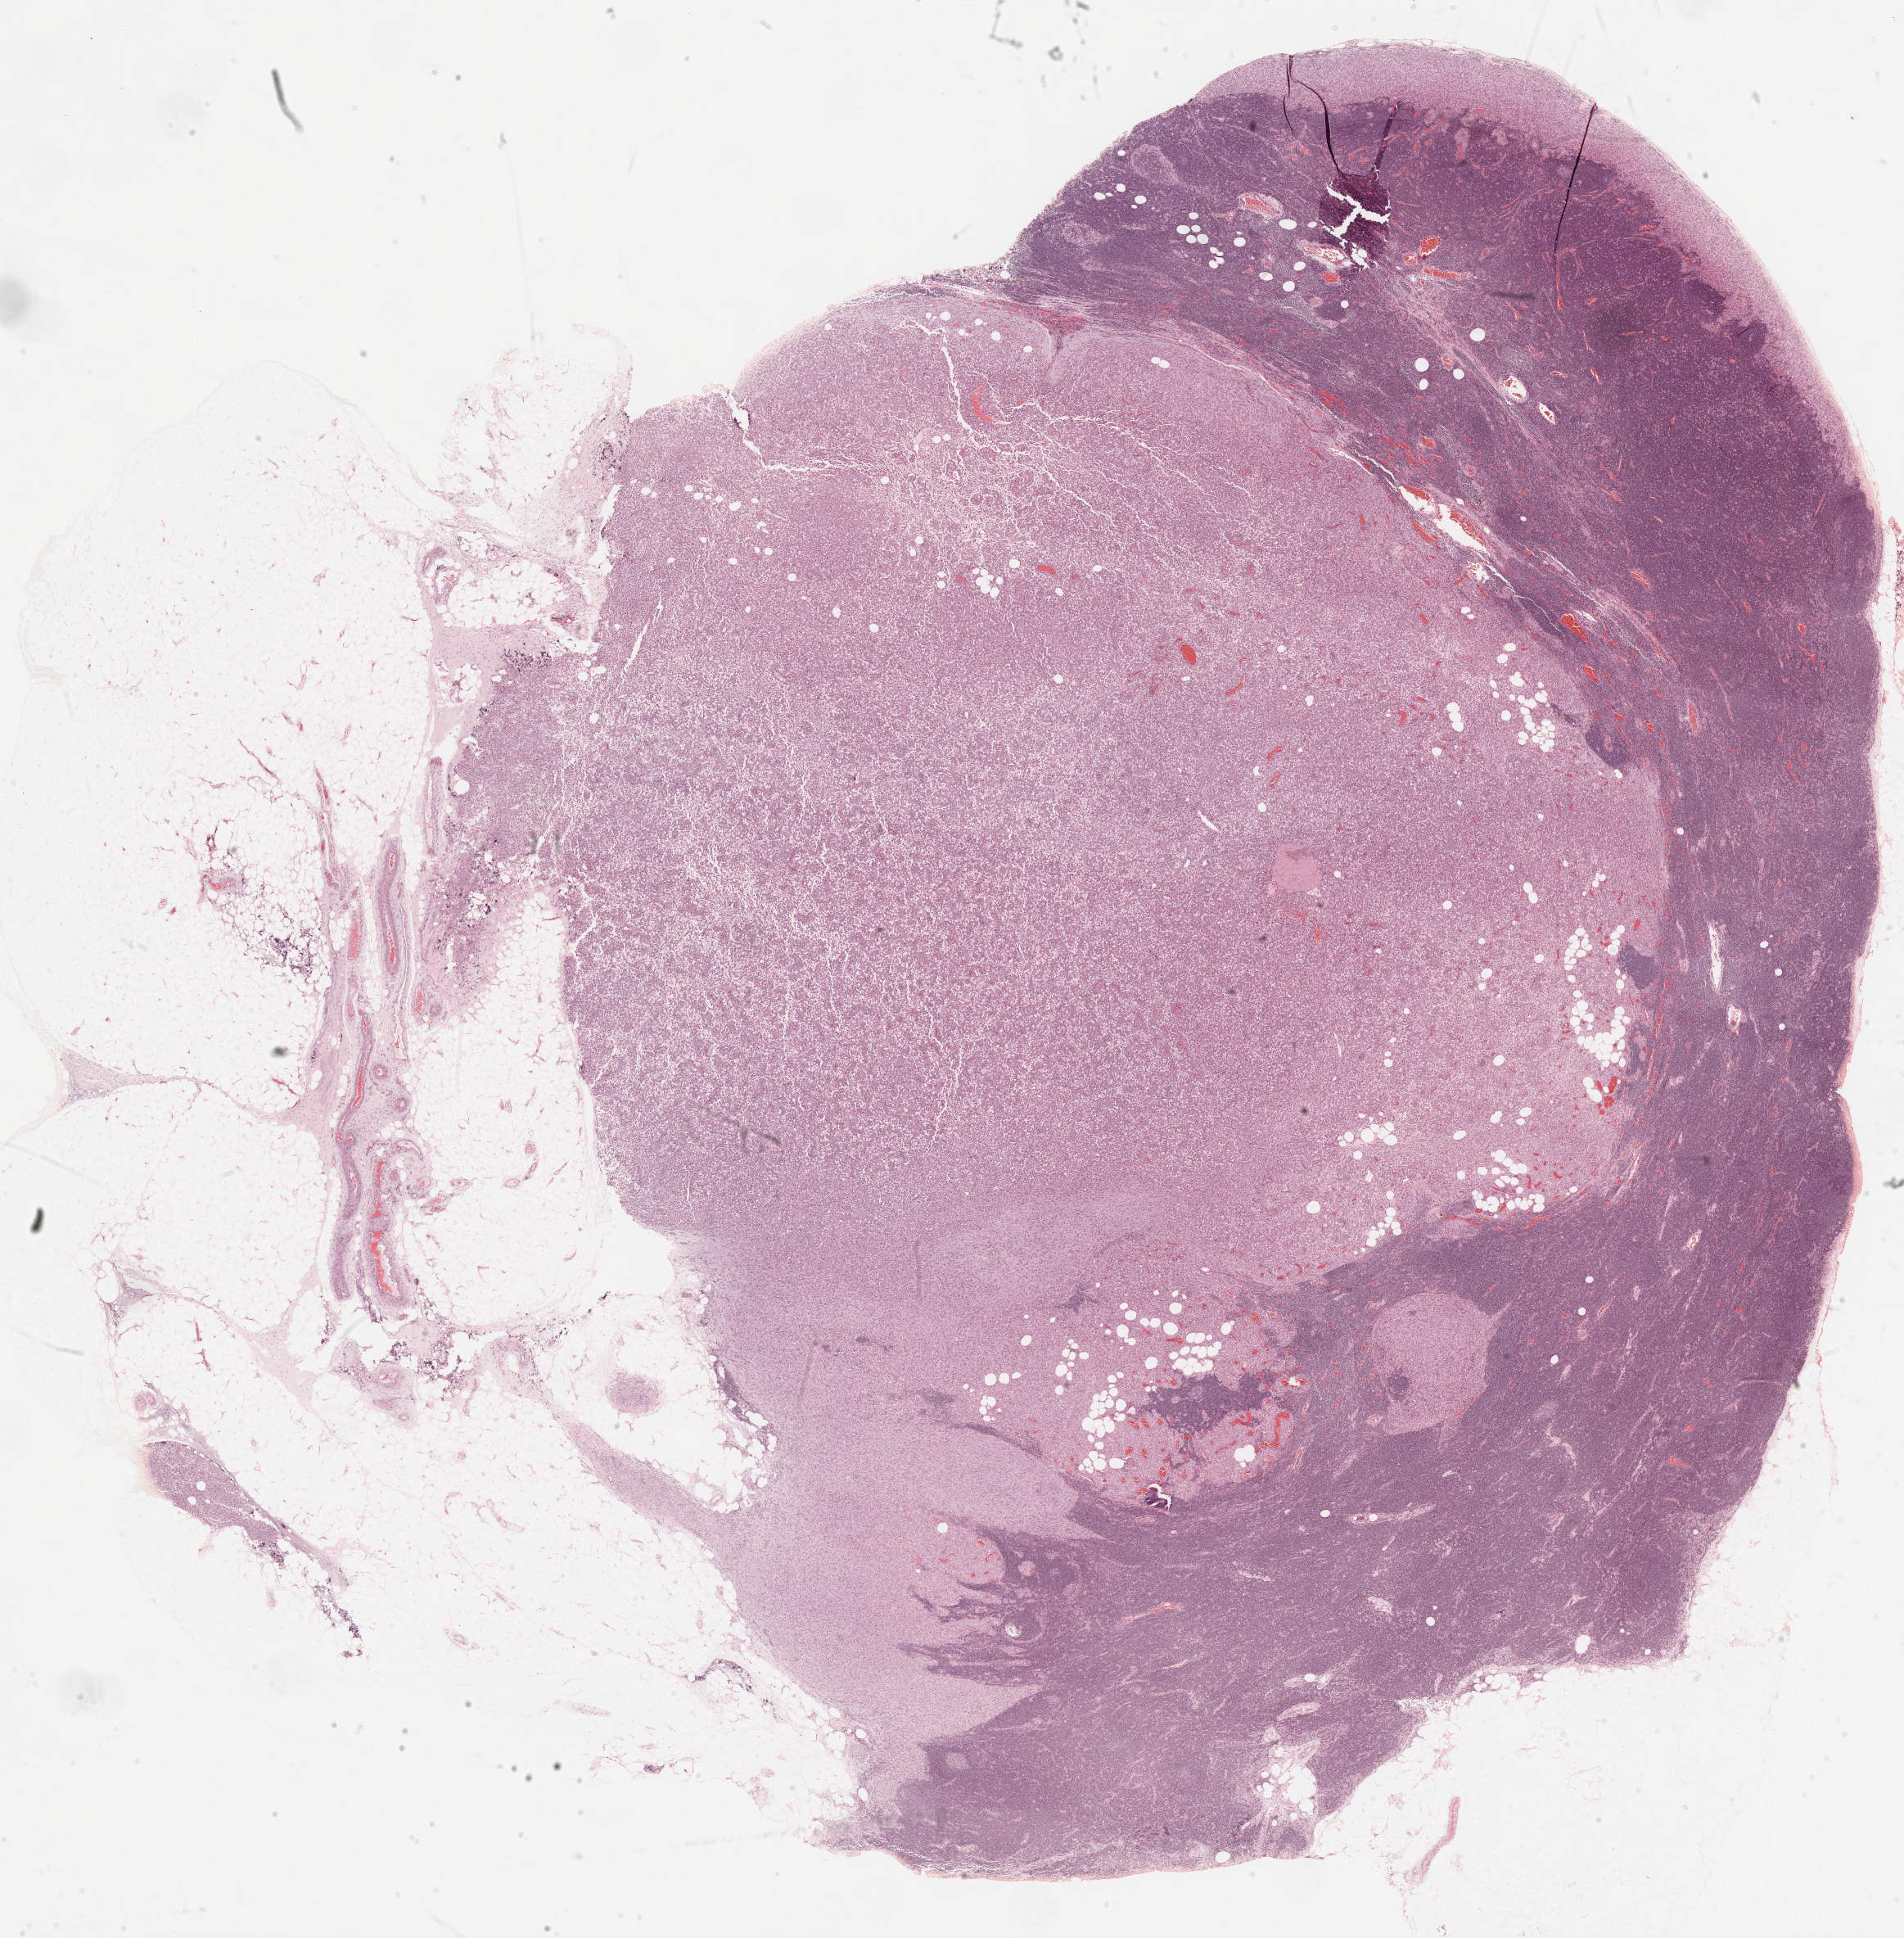
H&E whole-slide image, whole scanned area (about 18.8 x 19.1 mm, slide scanned at 20x) shown as a low-resolution overview. Formalin-fixed paraffin-embedded (FFPE) diagnostic section. Metastatic tumour sample, sampled site not recorded. Male, age 33 years at initial diagnosis.
This section: metastatic tumour tissue. Patient diagnosis: Malignant melanoma, NOS.